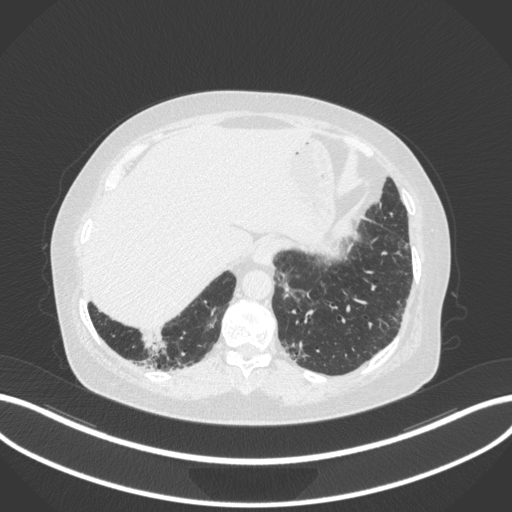
Chest CT, one axial slice. Position 16 of 303 along the scan axis. Reconstruction kernel B31f. Lung window (W 1500 / L -600 HU). 1 mm slice thickness. 512 × 512 image matrix, field of view 400 × 400 mm. Female patient, age 65 years. Case-level facts recorded for this patient, not image findings: clinical TNM (as recorded): T2b N1 M0; histopathological grade: G1.
Annotated regions visible in this slice (bounding box drawn by a radiologist):
- lung tumour (recorded histology: adenocarcinoma): bounding box <138,327,171,359> (left, top, right, bottom; pixels)